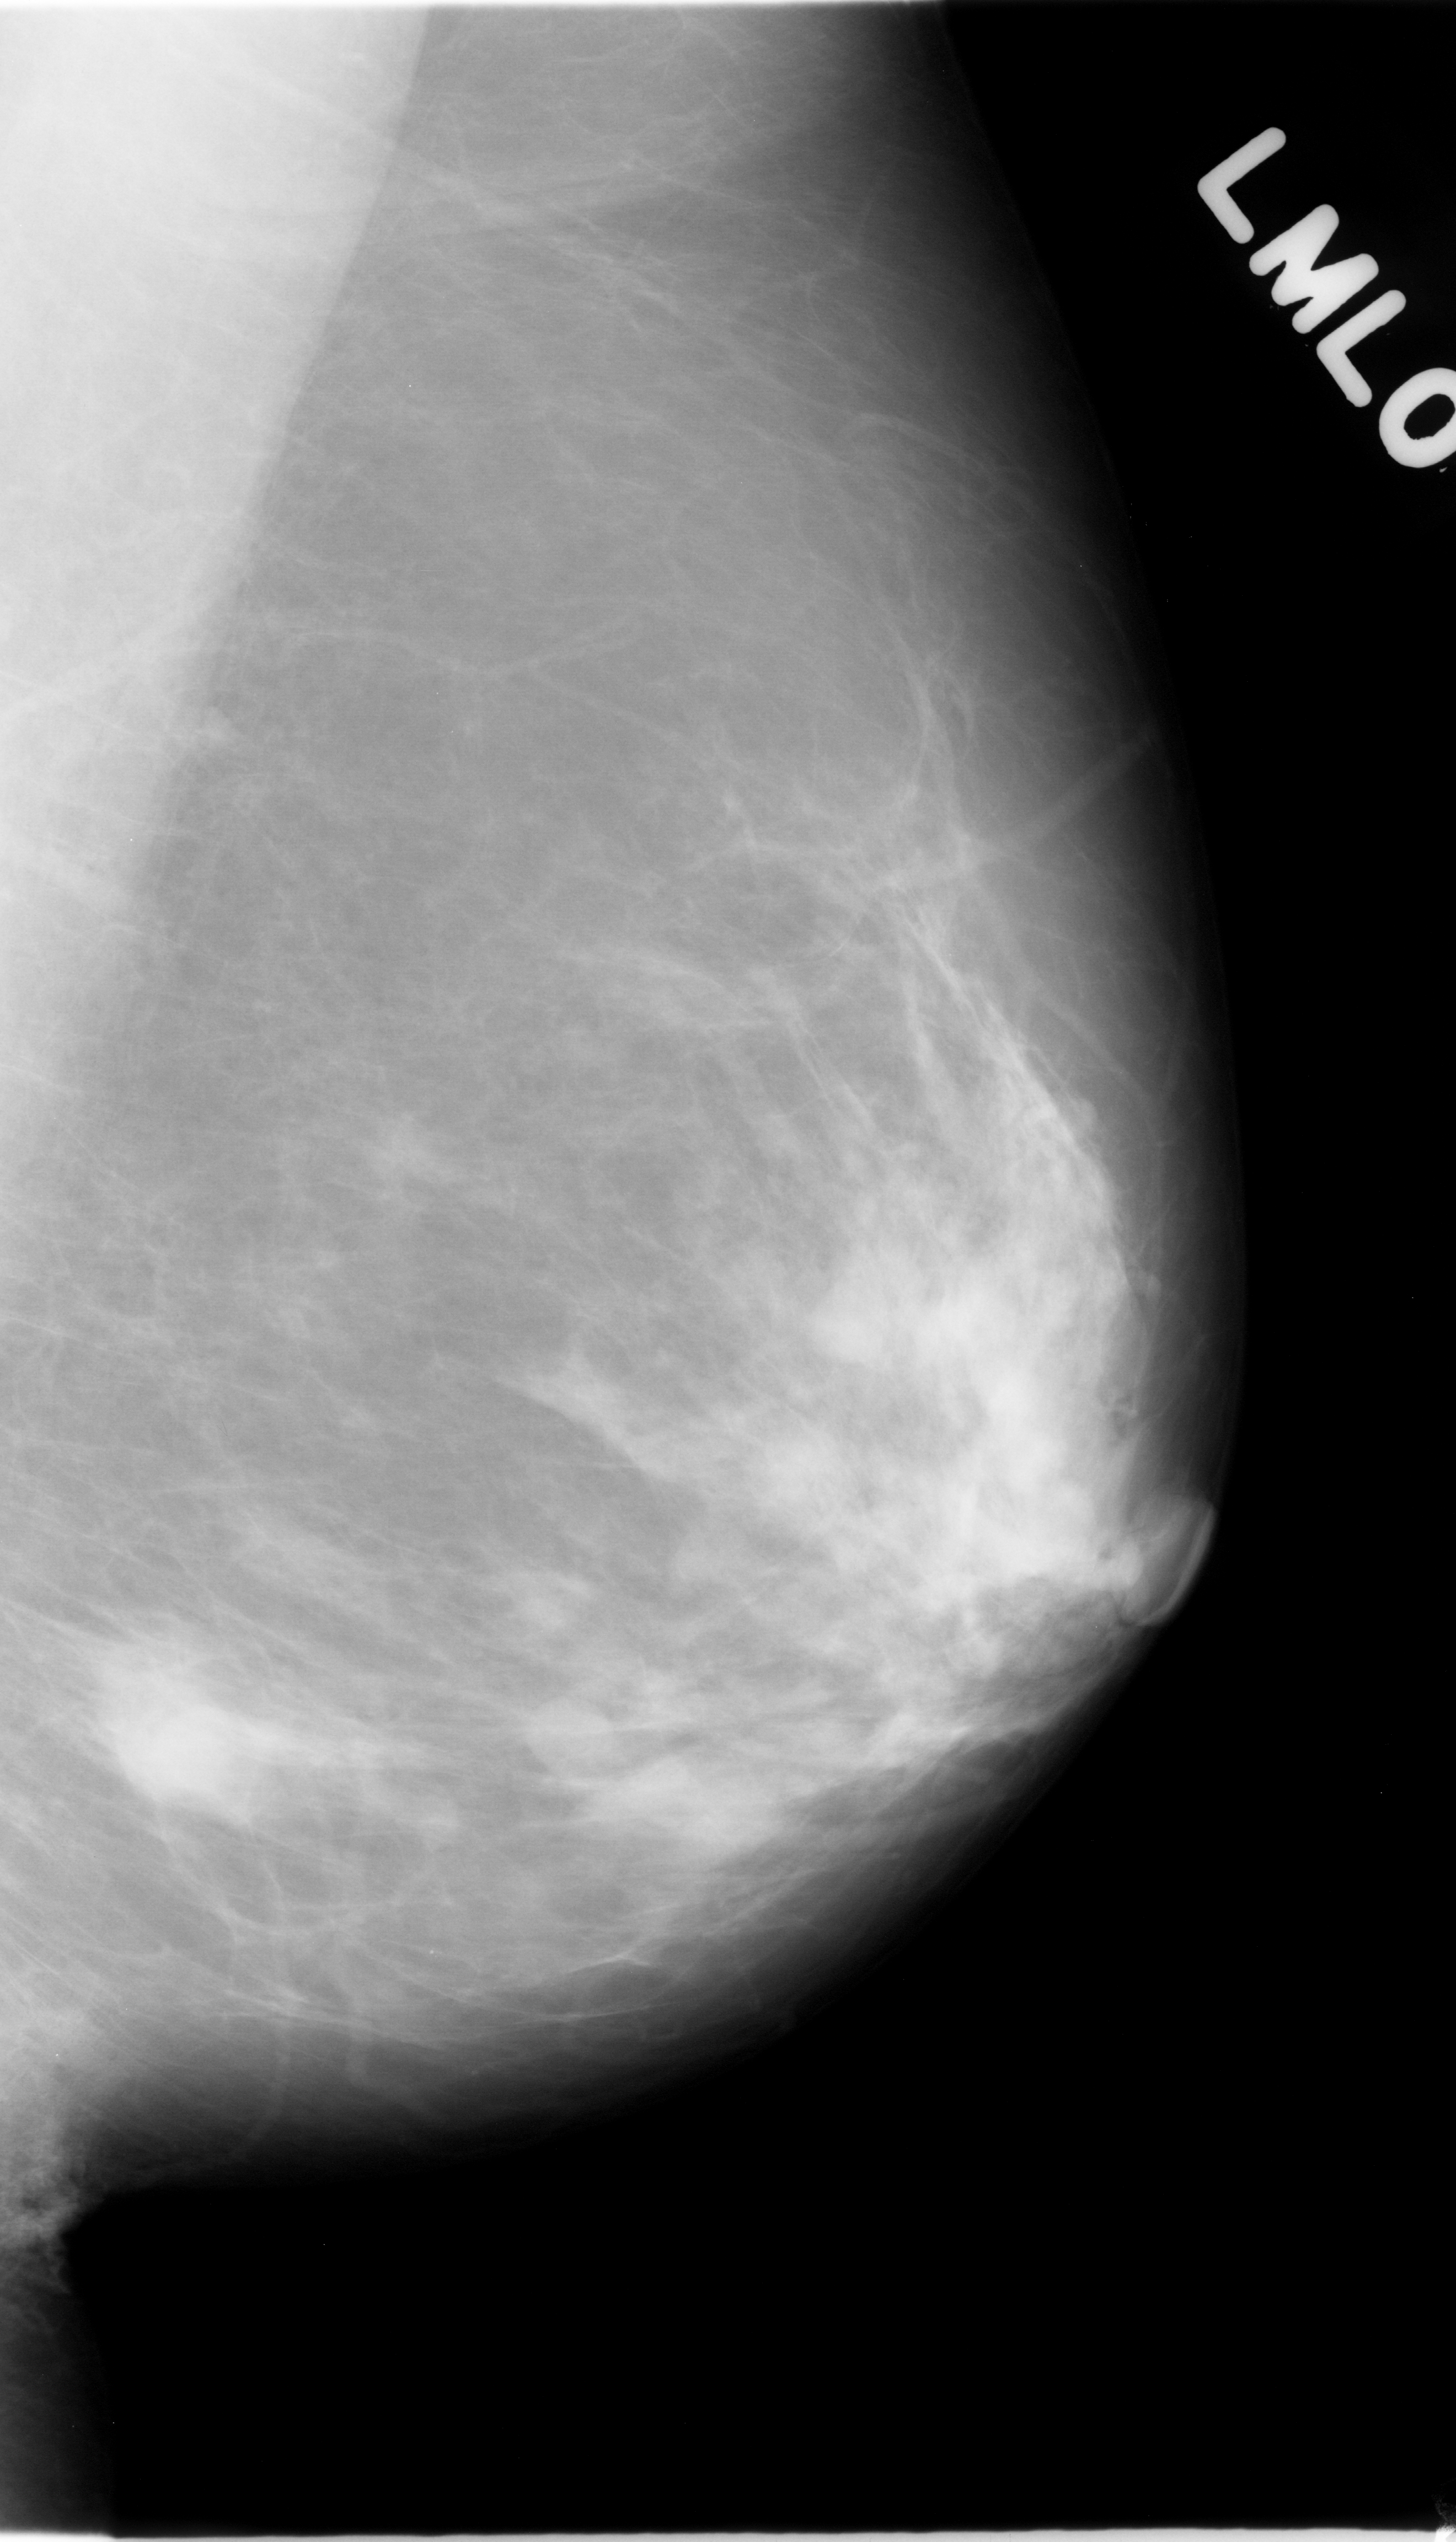
Digitized screen-film mammogram; left breast; MLO view; breast composition: scattered fibroglandular densities (BI-RADS density category 2 of 4); 1456 × 2542 image matrix.
Expert-marked regions of interest on this film, with their recorded descriptors:
- Finding 1 of 2: mass, margins ill defined; BI-RADS assessment category 5; subtlety rating 5 on a 1 (subtle) to 5 (obvious) scale; pathology result (as recorded, not read from the image): malignant: box from (x=84, y=1629) to (x=290, y=1828) px
- Finding 2 of 2: mass, shape oval, margins circumscribed; BI-RADS assessment category 3; subtlety rating 5 on a 1 (subtle) to 5 (obvious) scale; pathology result (as recorded, not read from the image): benign: (x=501, y=1696)–(x=637, y=1793)